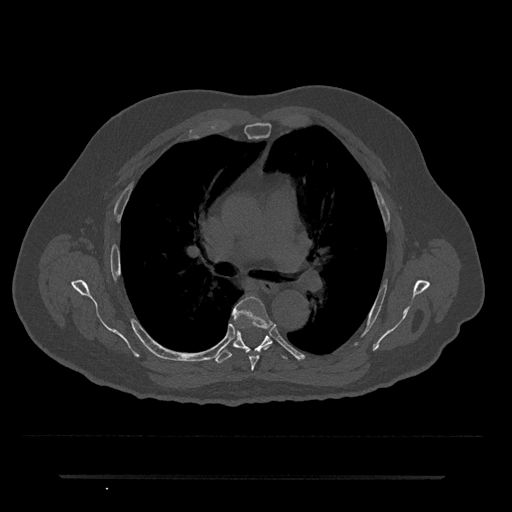
CT including the spine, one axial slice; 120 kVp; bone window (W 1800 / L 400 HU); 0.5 mm slice thickness; 512 × 512 image matrix, field of view 437 × 437 mm. Male patient, age 69 years. Case-level facts recorded for this patient, not image findings: primary cancer: prostate.
Structures marked on this image (semi-automatically segmented with operator editing):
- T5 vertebra: box from (x=232, y=296) to (x=272, y=371) px
- T6 vertebra: (x=215, y=320)–(x=287, y=363)